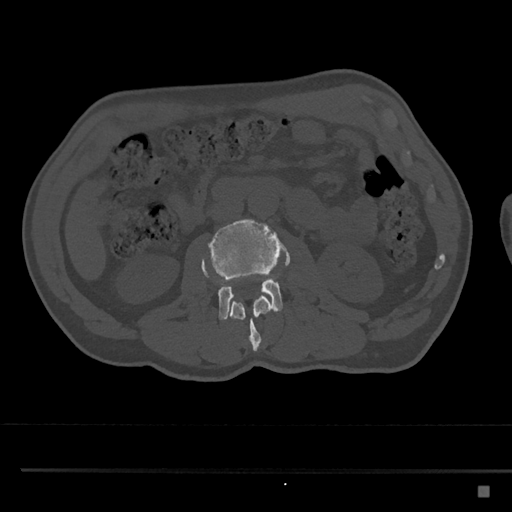
CT including the spine, one axial slice; position 724 of 797 along the scan axis; 120 kVp; bone window (W 1800 / L 400 HU); 0.5 mm slice thickness; 512 × 512 image matrix, field of view 391 × 391 mm. Male patient, age 59 years. From the clinical record (not read from this slice): primary cancer: prostate.
Annotated regions visible in this slice (semi-automatically segmented with operator editing):
- L2 vertebra: bounding box <202,260,272,351> (left, top, right, bottom; pixels)
- L3 vertebra: <201,219,290,320>